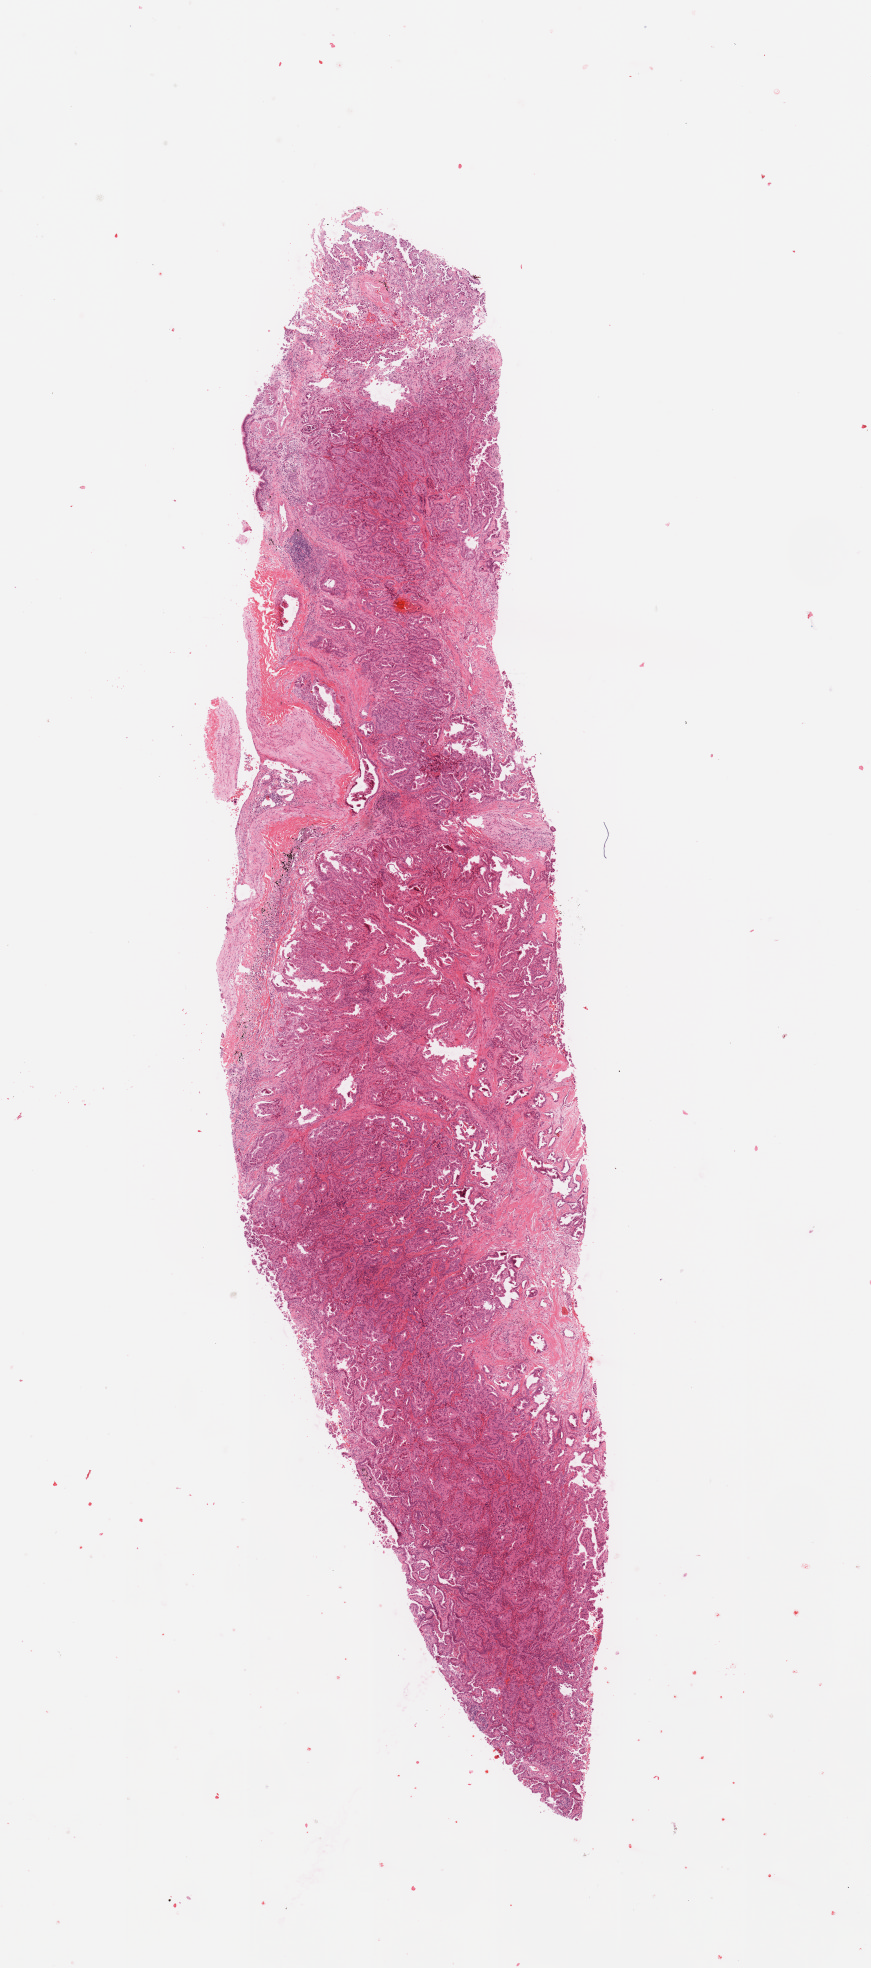
H&E whole-slide image — low-resolution overview of the scanned area, about 6.9 x 15.6 mm. Tumour tissue sample, sampled site: lung. Patient: male, age 51 years. Histologic grade: G2 (moderately differentiated). Slide review estimates, as recorded: tumour nuclei 85%, necrosis 0%.
* AJCC pathologic stage: IA3
* histologic diagnosis: Adenocarcinoma, NOS
* primary tumour site (as recorded): left lower lobe